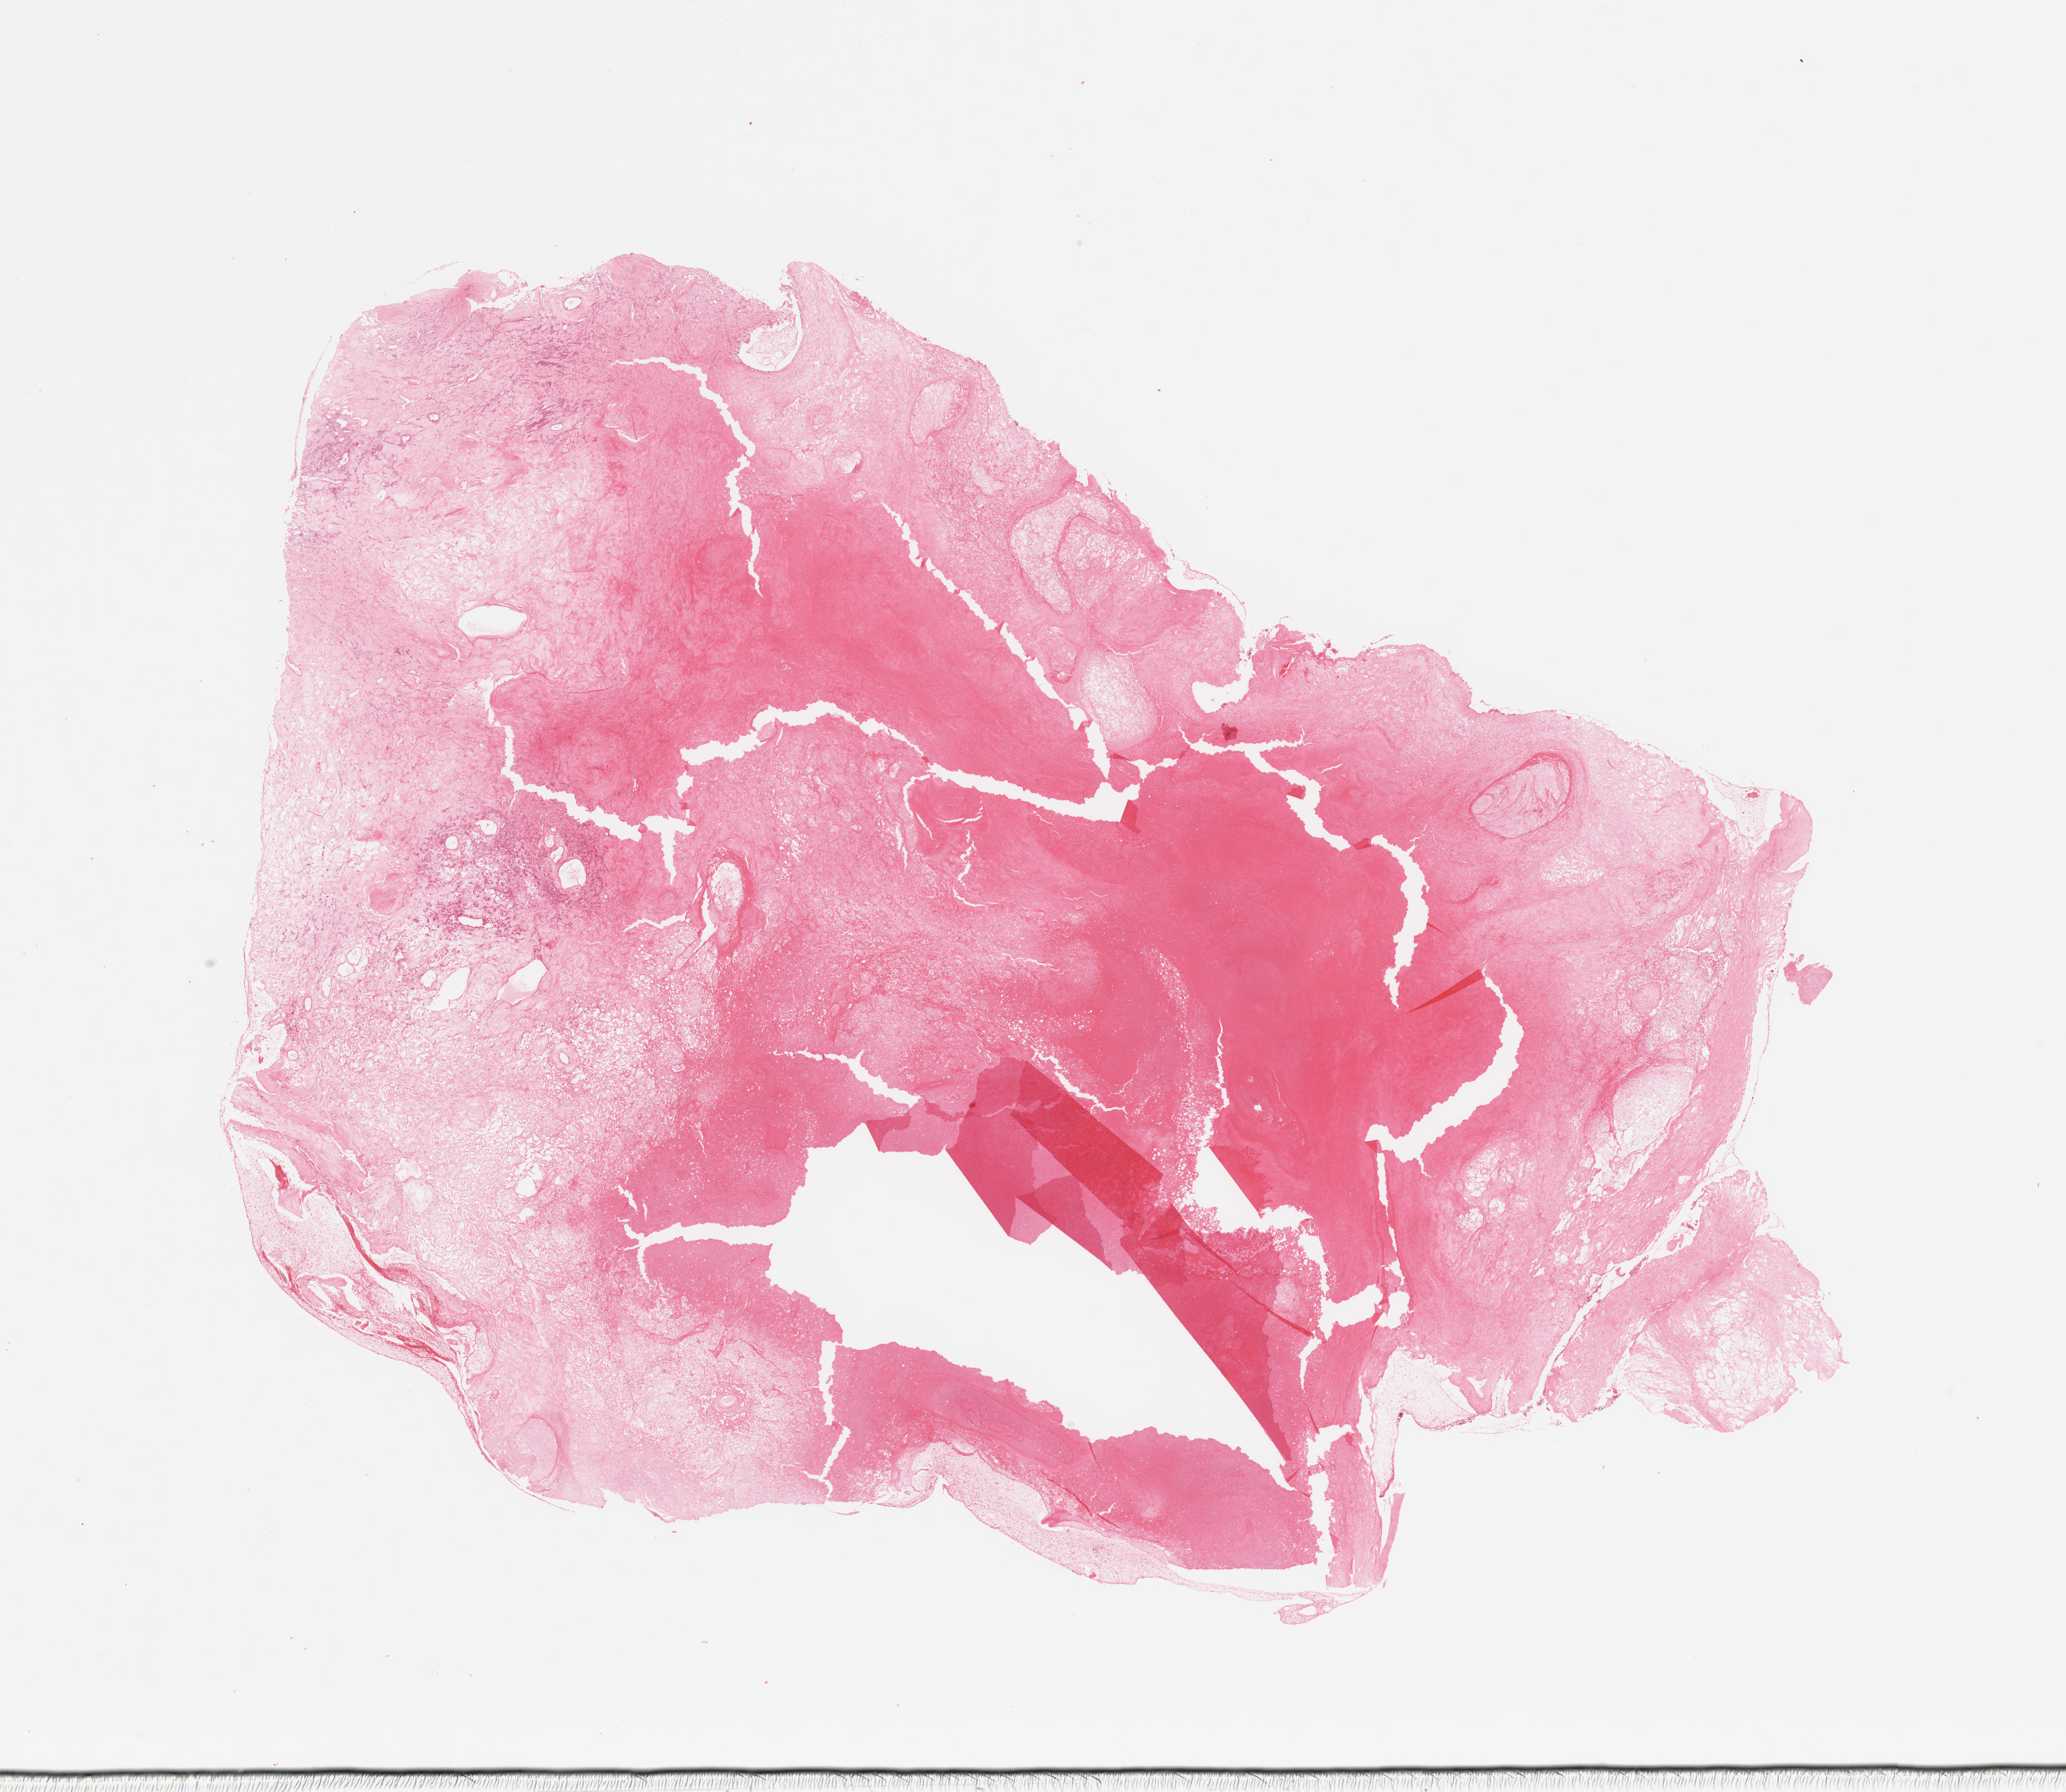
Digitized H&E tissue section (whole slide) — whole scanned area (about 23.6 x 20.5 mm, slide scanned at 20x) shown as a low-resolution overview. Tumour tissue sample, kidney. 68-year-old female patient. Histologic grade: G3 (poorly differentiated).
* diagnosis: Renal cell carcinoma, NOS